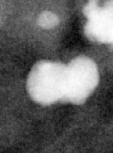
Cropped region of a digitized screen-film mammogram centred on a radiologist-marked abnormality; right breast; CC view; BI-RADS breast density category 2 (scale 1–4).
- Marked abnormality: calcifications, morphology pleomorphic / fine linear branching, distribution segmental; BI-RADS assessment category 5; subtlety rating 5 on a 1 (subtle) to 5 (obvious) scale; pathology (as recorded): malignant.